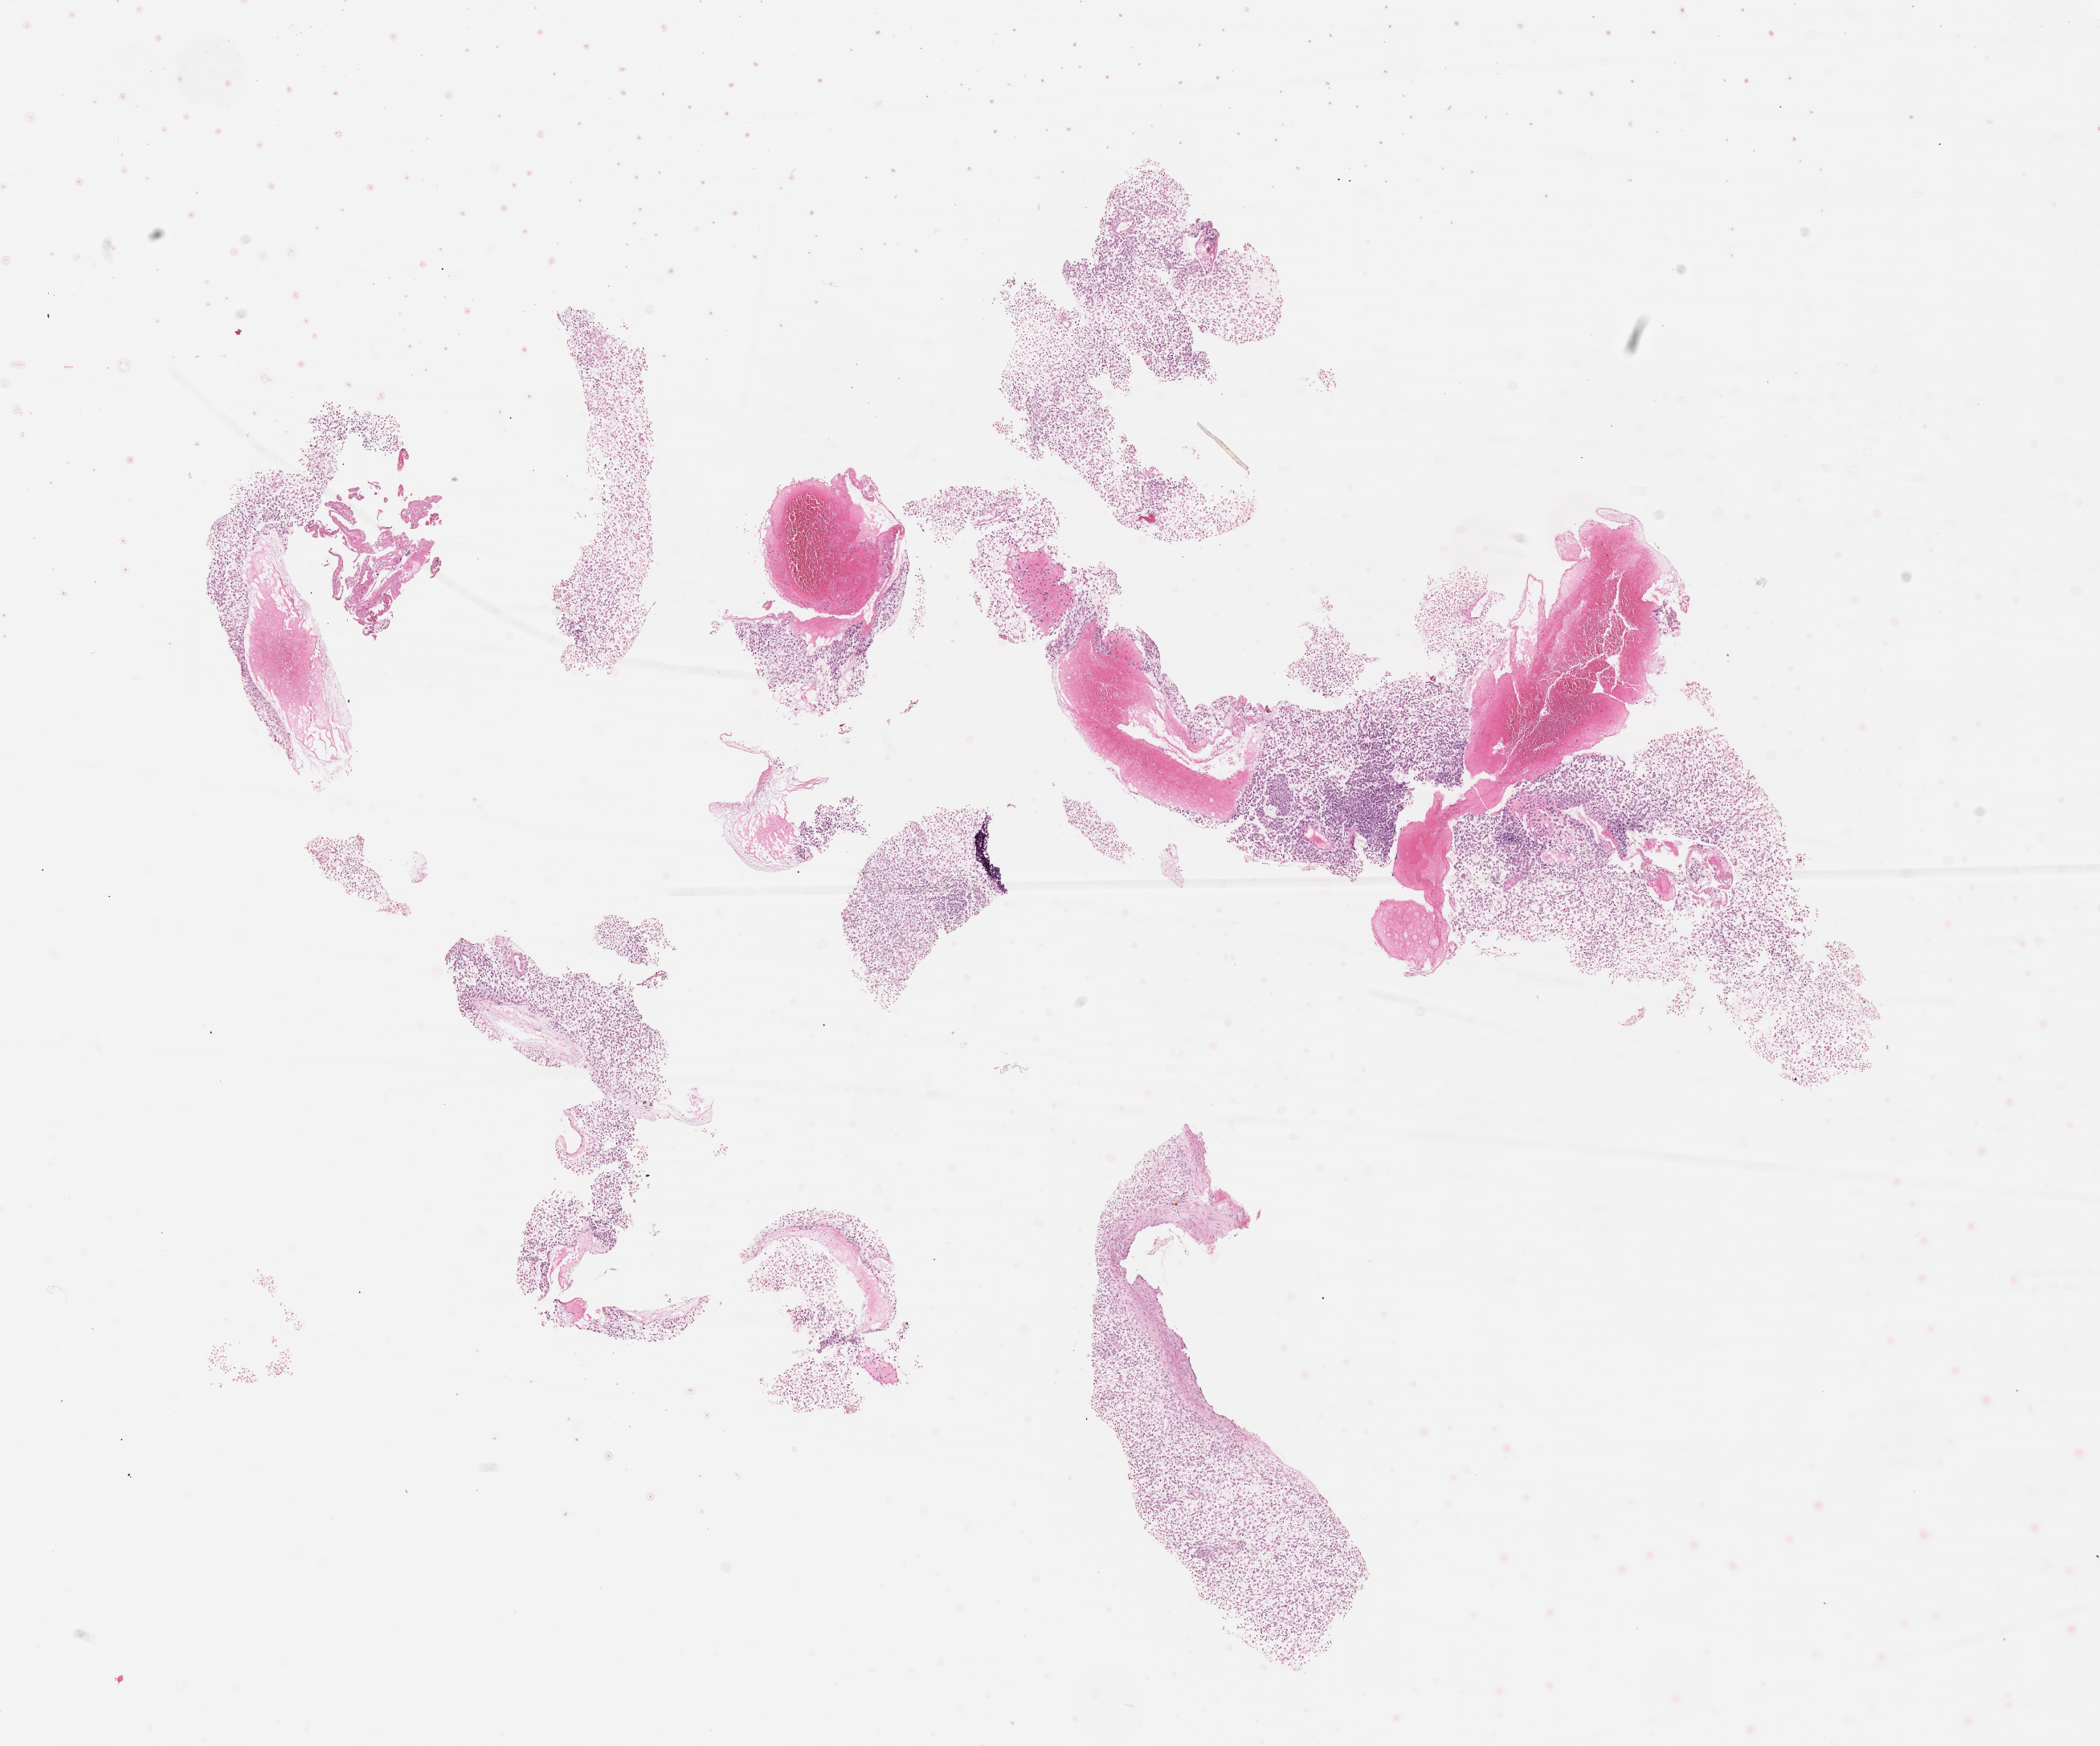
H&E whole-slide image of tumor tissue, shown as a low-resolution overview of the whole scanned area (about 10.6 x 8.8 mm), formalin-fixed, paraffin-embedded (FFPE) tissue, site: prostate-peri. Male patient, age at diagnosis 16.2 years.
Metastatic status at presentation (as recorded): non-metastatic. Diagnosis: rhabdomyosarcoma; histological classification: embryonal rhabdomyosarcoma. Stage (as recorded): 3.